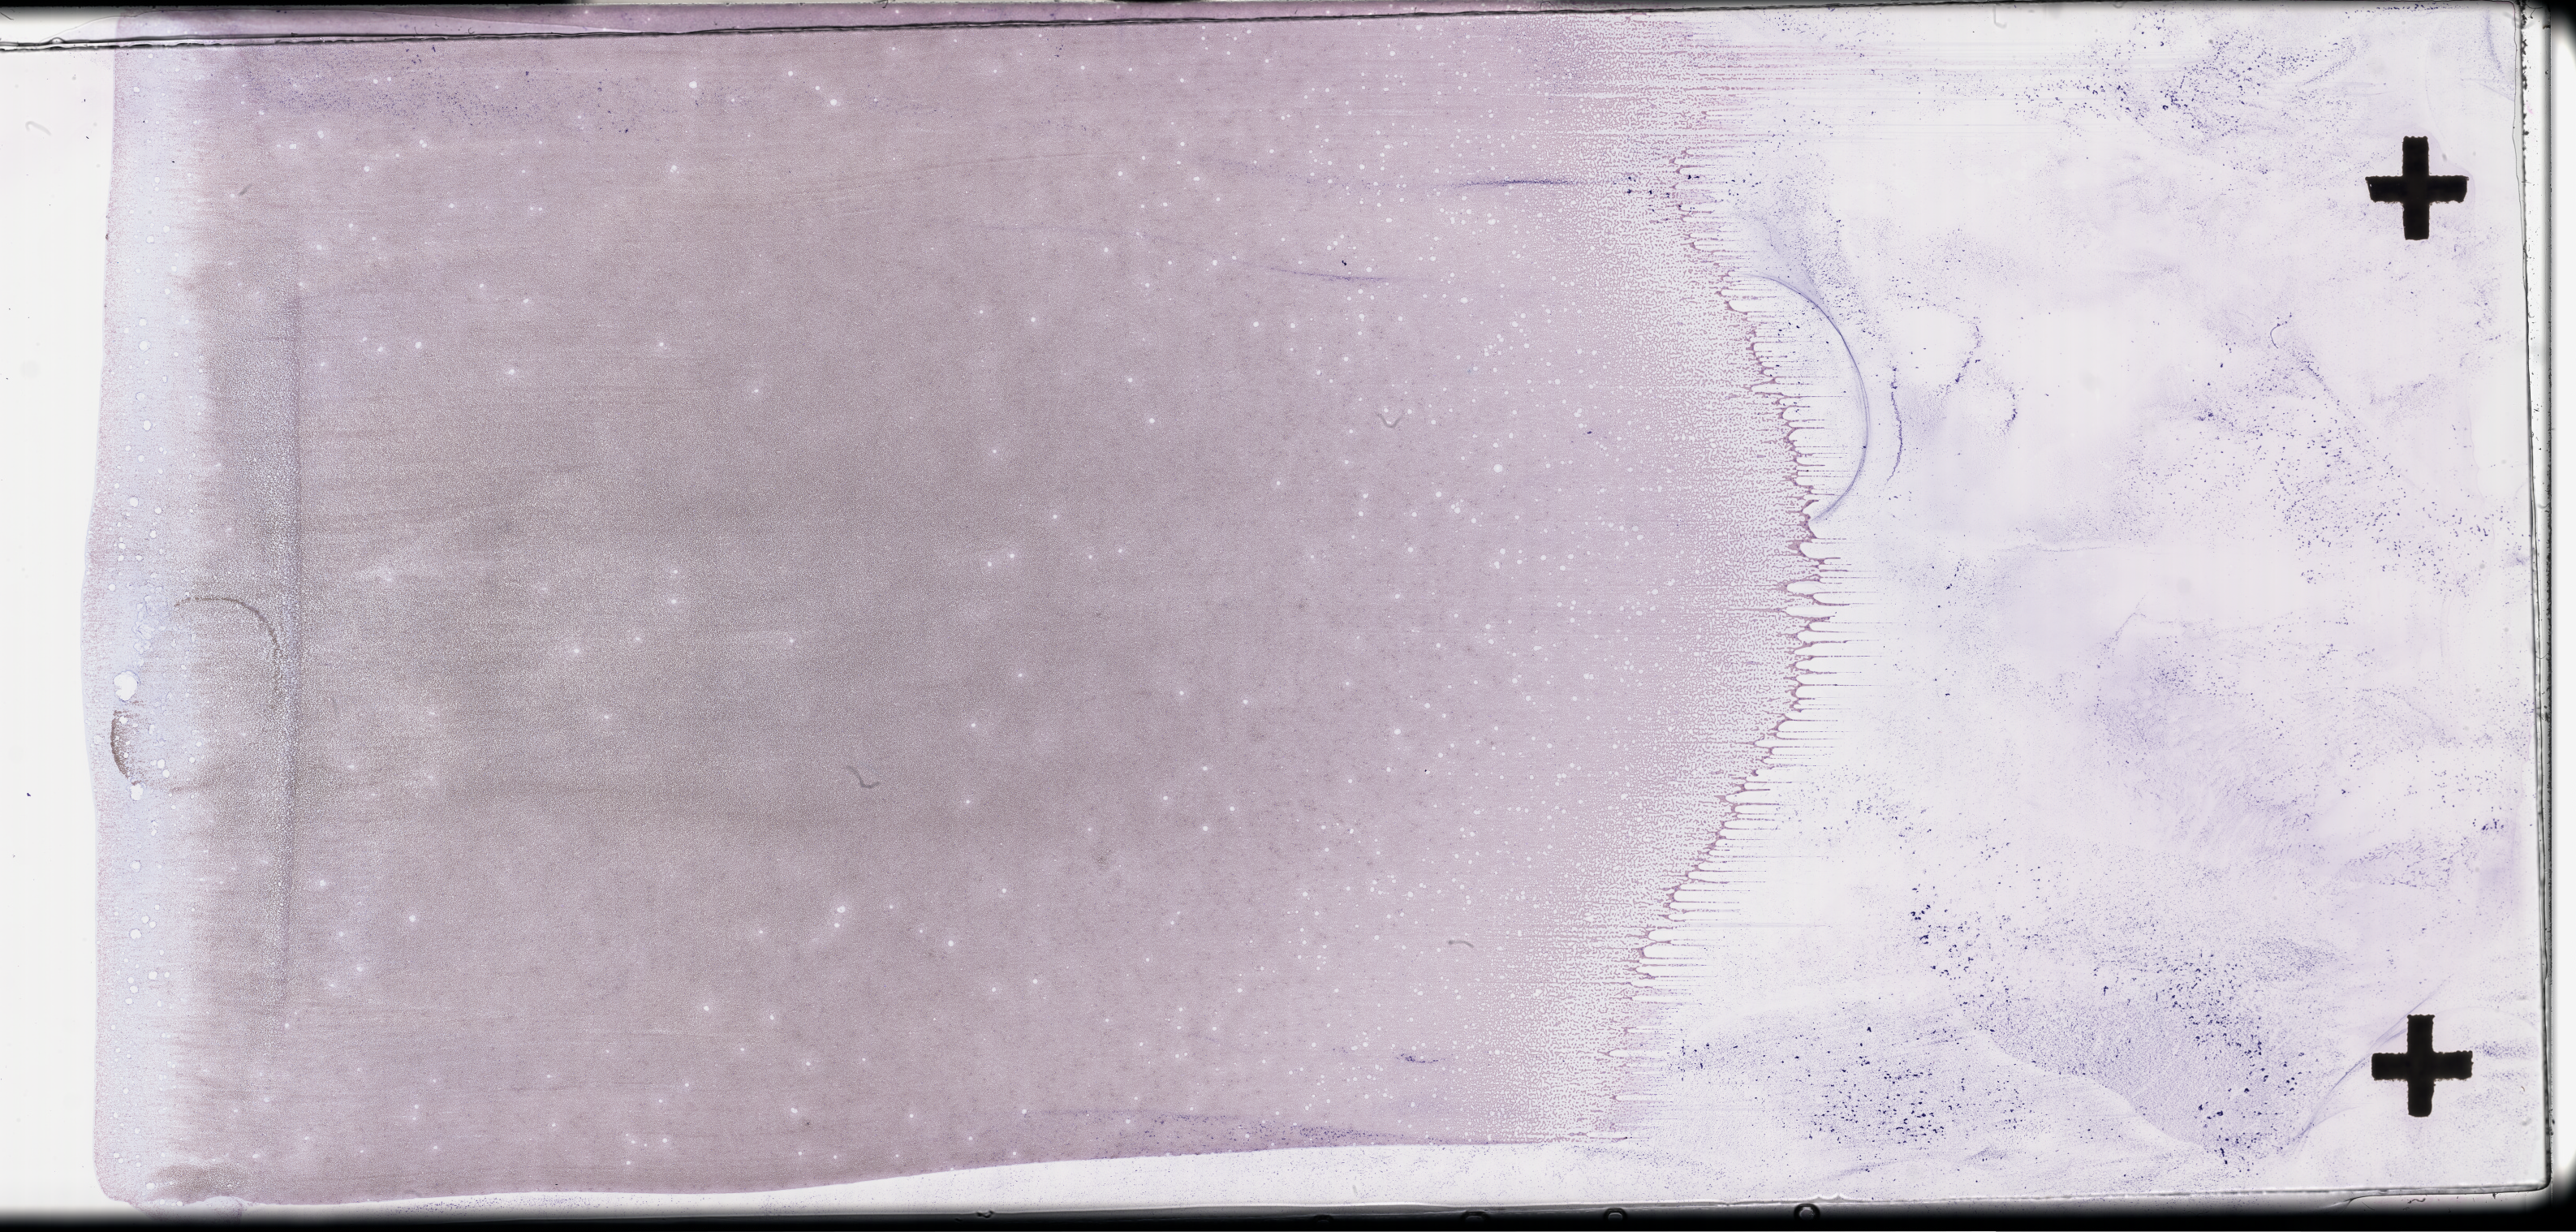
Wright-Giemsa-stained whole blood smear, whole-slide image — a low-resolution overview of the entire scanned area, about 51.3 x 24.5 mm, smear from an EDTA sample, specimen time point: collected on treatment. Female patient.
• from a patient with: Plasma Cell Myeloma